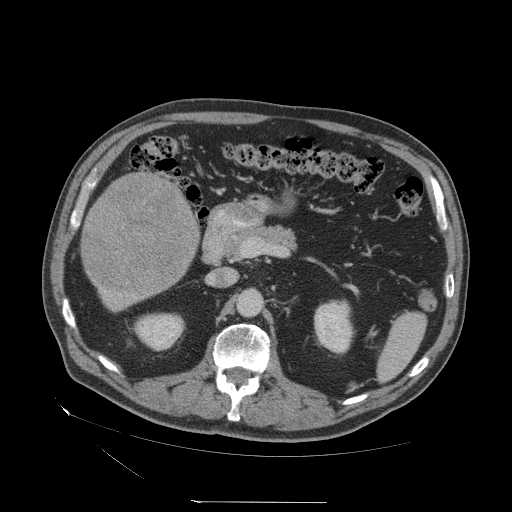
Contrast-enhanced abdominal CT (liver protocol), one axial slice; slice 16 of 83 in the series (ordered by position); 140 kVp; soft-tissue window (W 400 / L 40 HU); 2.5 mm slice thickness; 512 × 512 image matrix, field of view 460 × 460 mm. Case-level facts recorded for this patient, not image findings: diagnosis: hepatocellular carcinoma (patient treated with transarterial chemoembolisation; whether this scan precedes or follows treatment is not stated here); TNM stage (as recorded): Stage-I; Child-Pugh class: A; tumour differentiation: well differentiated; tumour nodularity: uninodular.
Annotated regions visible in this slice (semi-automatic segmentation, software-assisted and operator-edited):
- liver parenchyma outside the tumour (the mass and vessels are separate outlines, so this box may not span the whole liver): bounding box (x1, y1, x2, y2) in pixels: (82, 172, 200, 310)
- mass: (83, 175, 195, 291)